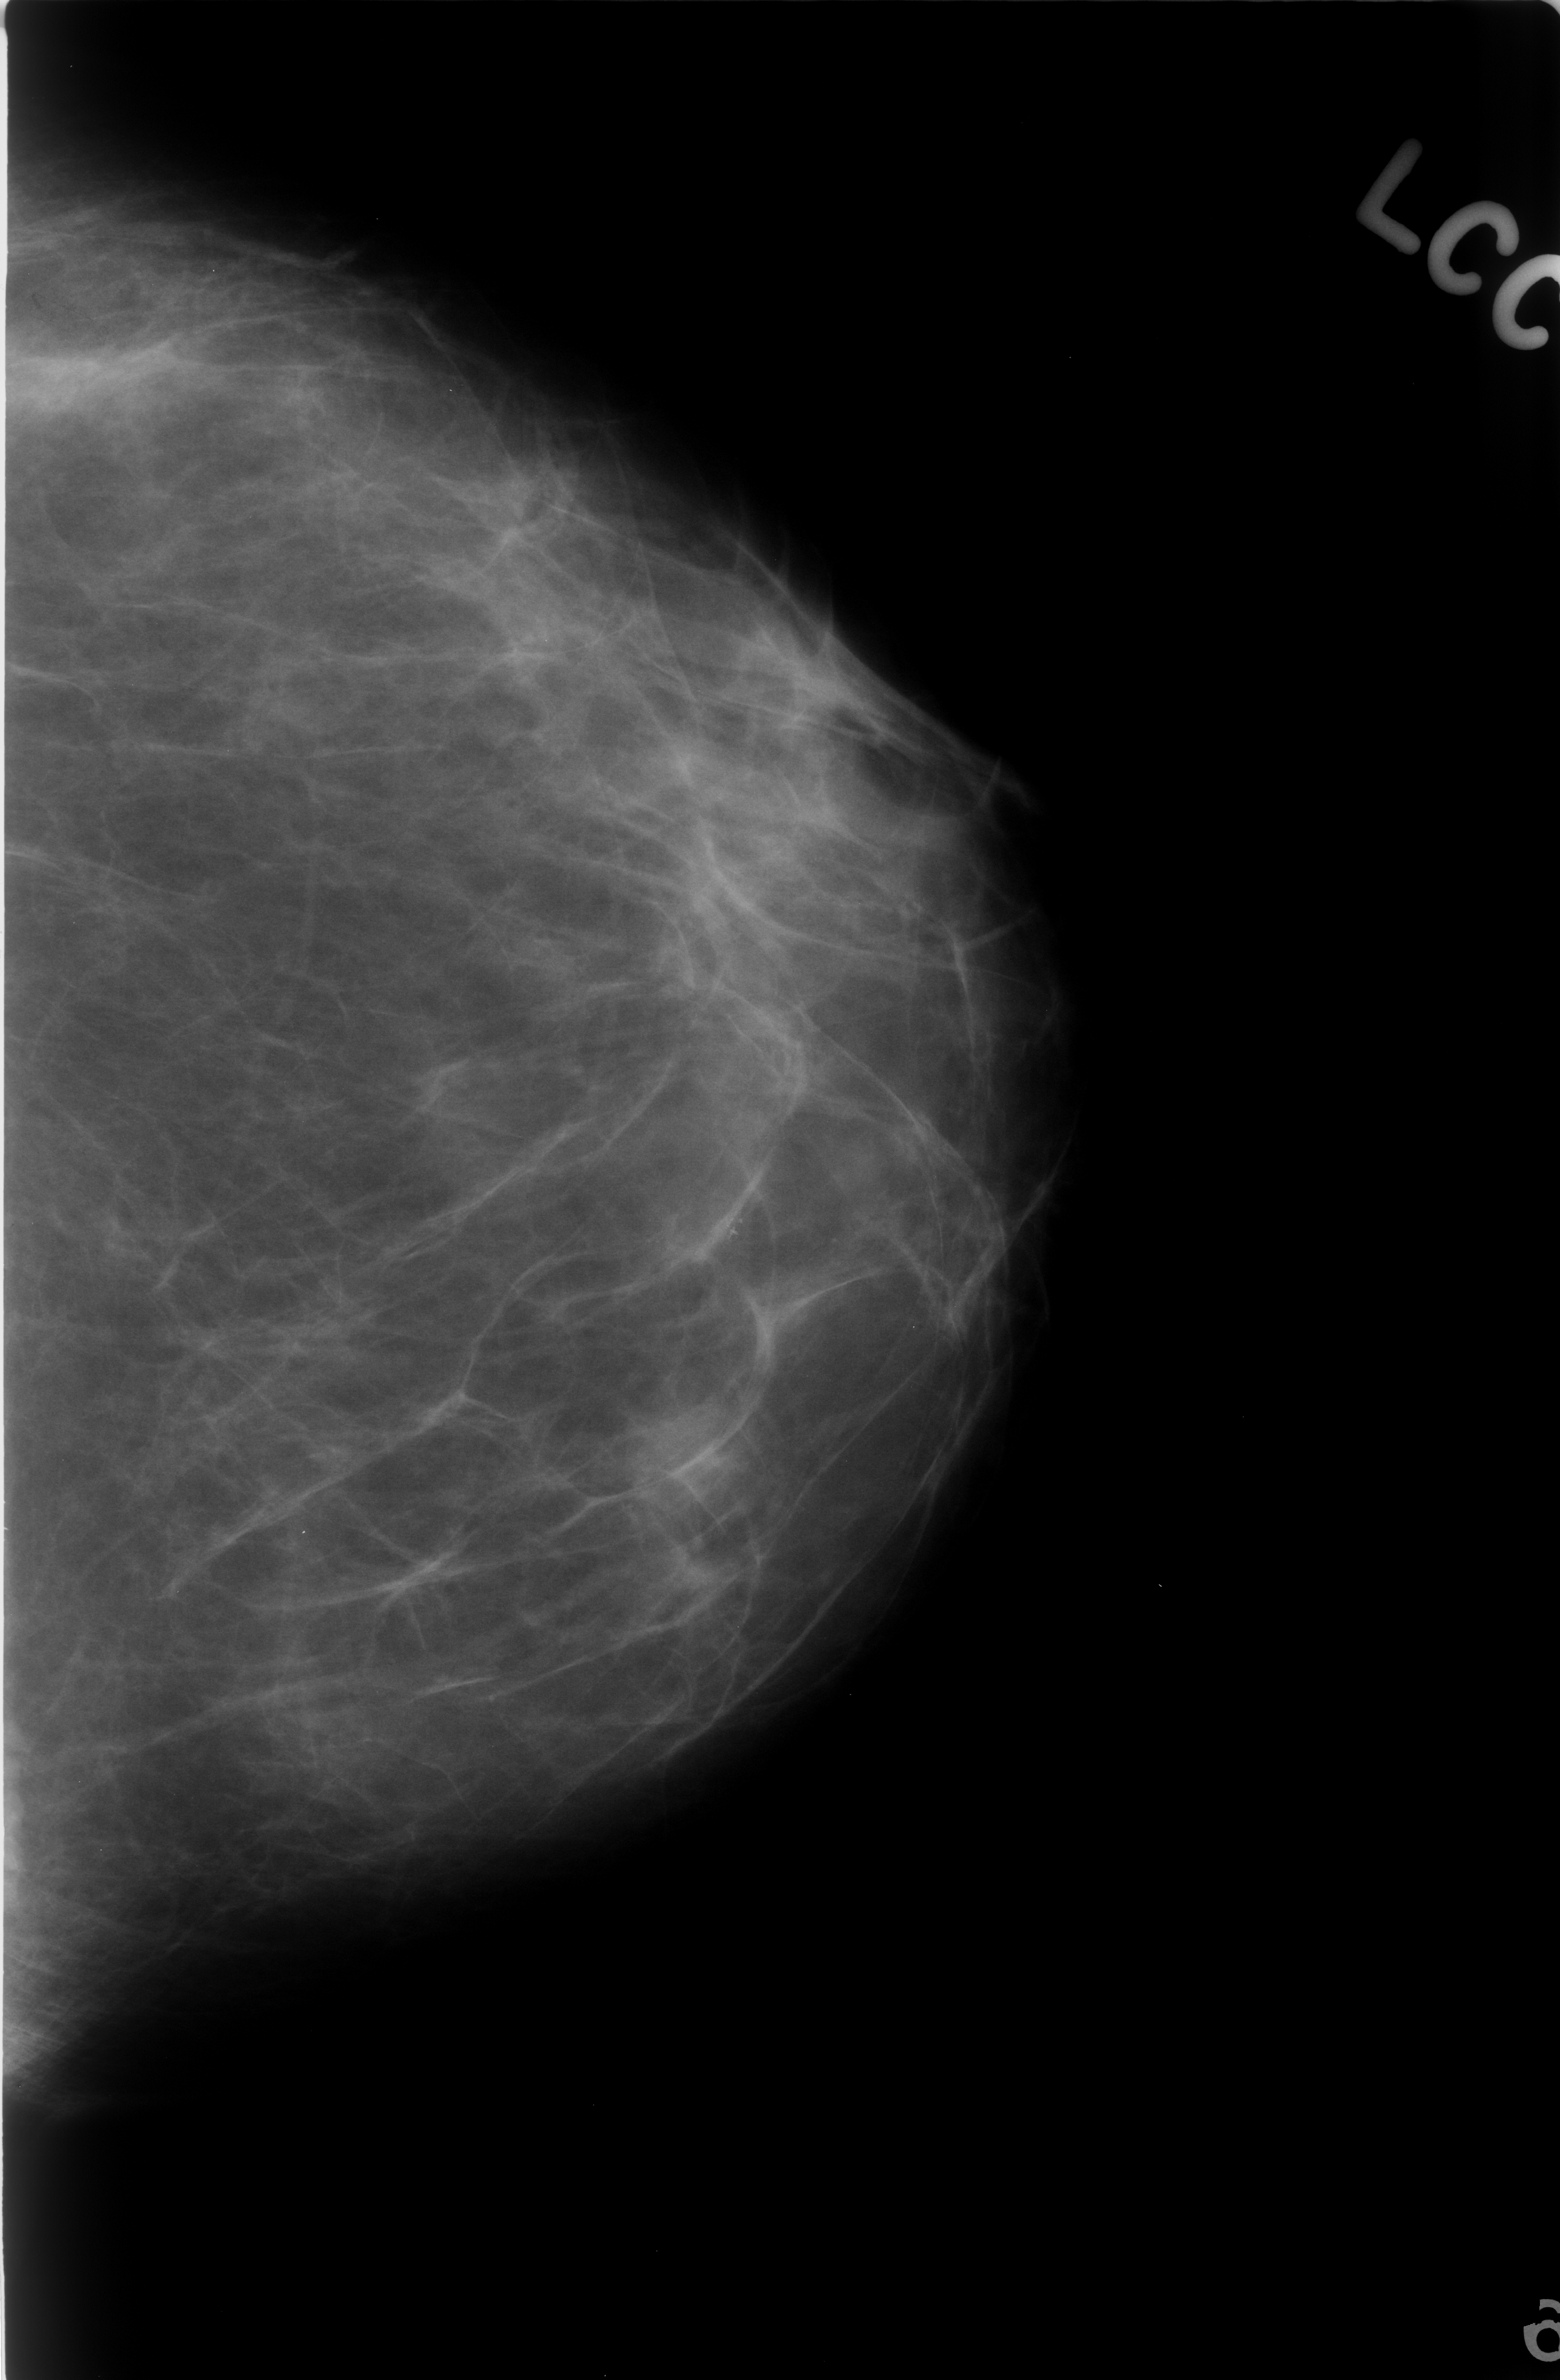
Mammogram (digitized film); left breast; CC view; BI-RADS breast density category 1 (scale 1–4).
Abnormality record for this image: calcifications, morphology pleomorphic, distribution clustered; BI-RADS assessment category 3; subtlety rating 3 on a 1 (subtle) to 5 (obvious) scale; pathology result (as recorded, not read from the image): benign.